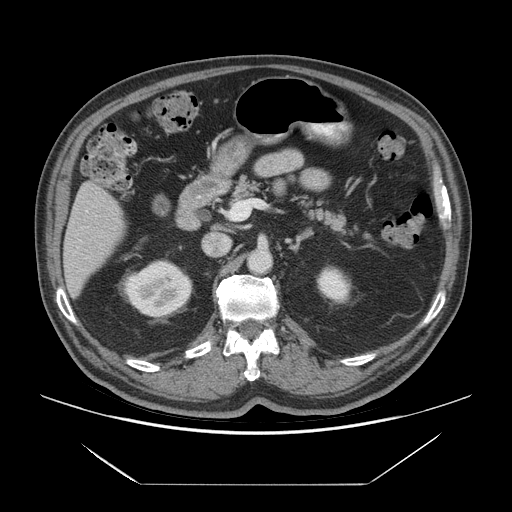
Contrast-enhanced abdominal CT (liver protocol), one axial slice. Slice 29 of 75 in the series (ordered by position). Reconstruction kernel STANDARD. Soft-tissue window (W 400 / L 40 HU). 2.5 mm slice thickness. 512 × 512 image matrix, field of view 420 × 420 mm. From the clinical record (not read from this slice): diagnosis: hepatocellular carcinoma (patient treated with transarterial chemoembolisation; whether this scan precedes or follows treatment is not stated here); TNM stage (as recorded): Stage-I; Child-Pugh class: A; tumour nodularity: uninodular; tumour size: 5.8 cm.
Structures marked on this image (semi-automatic segmentation, software-assisted and operator-edited):
- liver parenchyma outside the tumour (the mass and vessels are separate outlines, so this box may not span the whole liver): bounding box <62,182,124,298> (left, top, right, bottom; pixels)